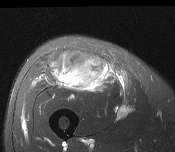
MRI of an extremity soft-tissue mass, one axial slice. Slice 72 of 116 in the series (ordered by position). T2-weighted fat-saturated. MR volume resampled by the dataset authors to the PET/CT grid (not the native acquisition matrix). 3.27 mm slice thickness. 175 × 152 image matrix, field of view 171 × 148 mm. Male patient. From the clinical record (not read from this slice): histological type: pleiomorphic leiomyosarcoma; grade: intermediate; site of the primary tumour: right thigh.
Outlined on this slice (expert contour drawn on MRI and transferred to this co-registered scan by the dataset authors):
- gross tumour volume including surrounding oedema: bounding box (x1, y1, x2, y2) in pixels: (54, 52, 109, 91)
- gross tumour volume (mass): (60, 58, 105, 89)